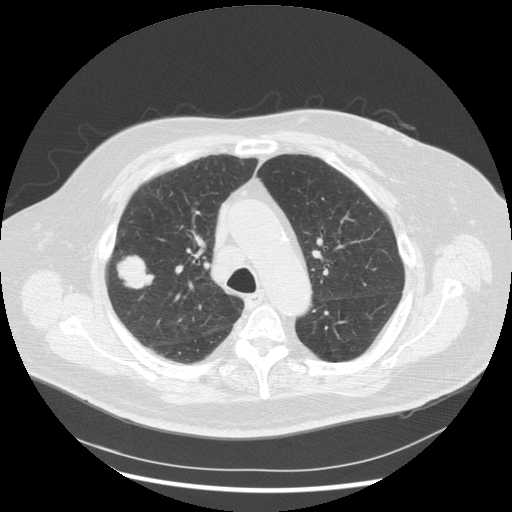
Low-dose screening chest CT, one axial slice. Position 197 of 263 along the scan axis. Reconstruction kernel STANDARD. 120 kVp. Lung window (W 1500 / L -600 HU). 2.5 mm slice thickness. 512 × 512 image matrix, field of view 400 × 400 mm.
Structures marked on this image (manually delineated by an expert):
- lesion 1 (tumor, upper lobe of right lung): bounding box [x1, y1, x2, y2] px = [117, 256, 154, 289]